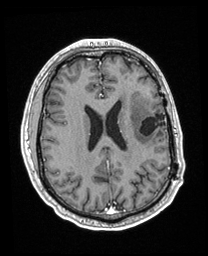
Brain MRI from a brain-tumour surgery series, one axial slice. Position 87 of 208 along the scan axis. T1-weighted post-contrast. 208 × 256 image matrix, field of view 211 × 260 mm. Case-level facts recorded for this patient, not image findings: histopathology: Astrocytoma; WHO grade: 3; IDH mutation: yes.
Outlined on this slice (manually delineated by an expert):
- previous resection cavity: bounding box [x1, y1, x2, y2] px = [140, 114, 166, 136]